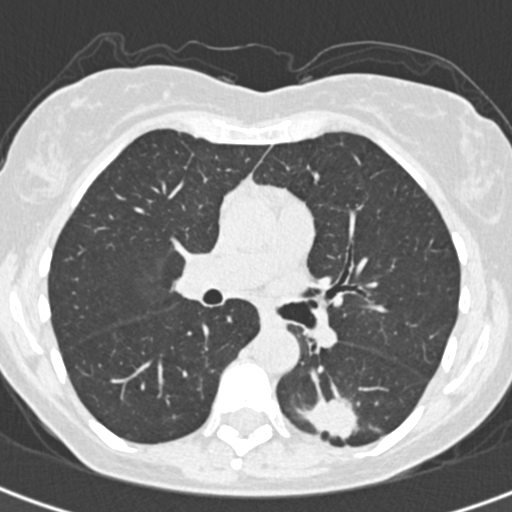
Low-dose screening chest CT, one axial slice; slice 196 of 328 in the series (ordered by position); 120 kVp; lung window (W 1500 / L -600 HU); 1 mm slice thickness; 512 × 512 image matrix.
Outlined on this slice (manually delineated by an expert):
- lesion 1 (tumor, lower lobe of left lung): bounding box (x1, y1, x2, y2) in pixels: (303, 399, 357, 439)